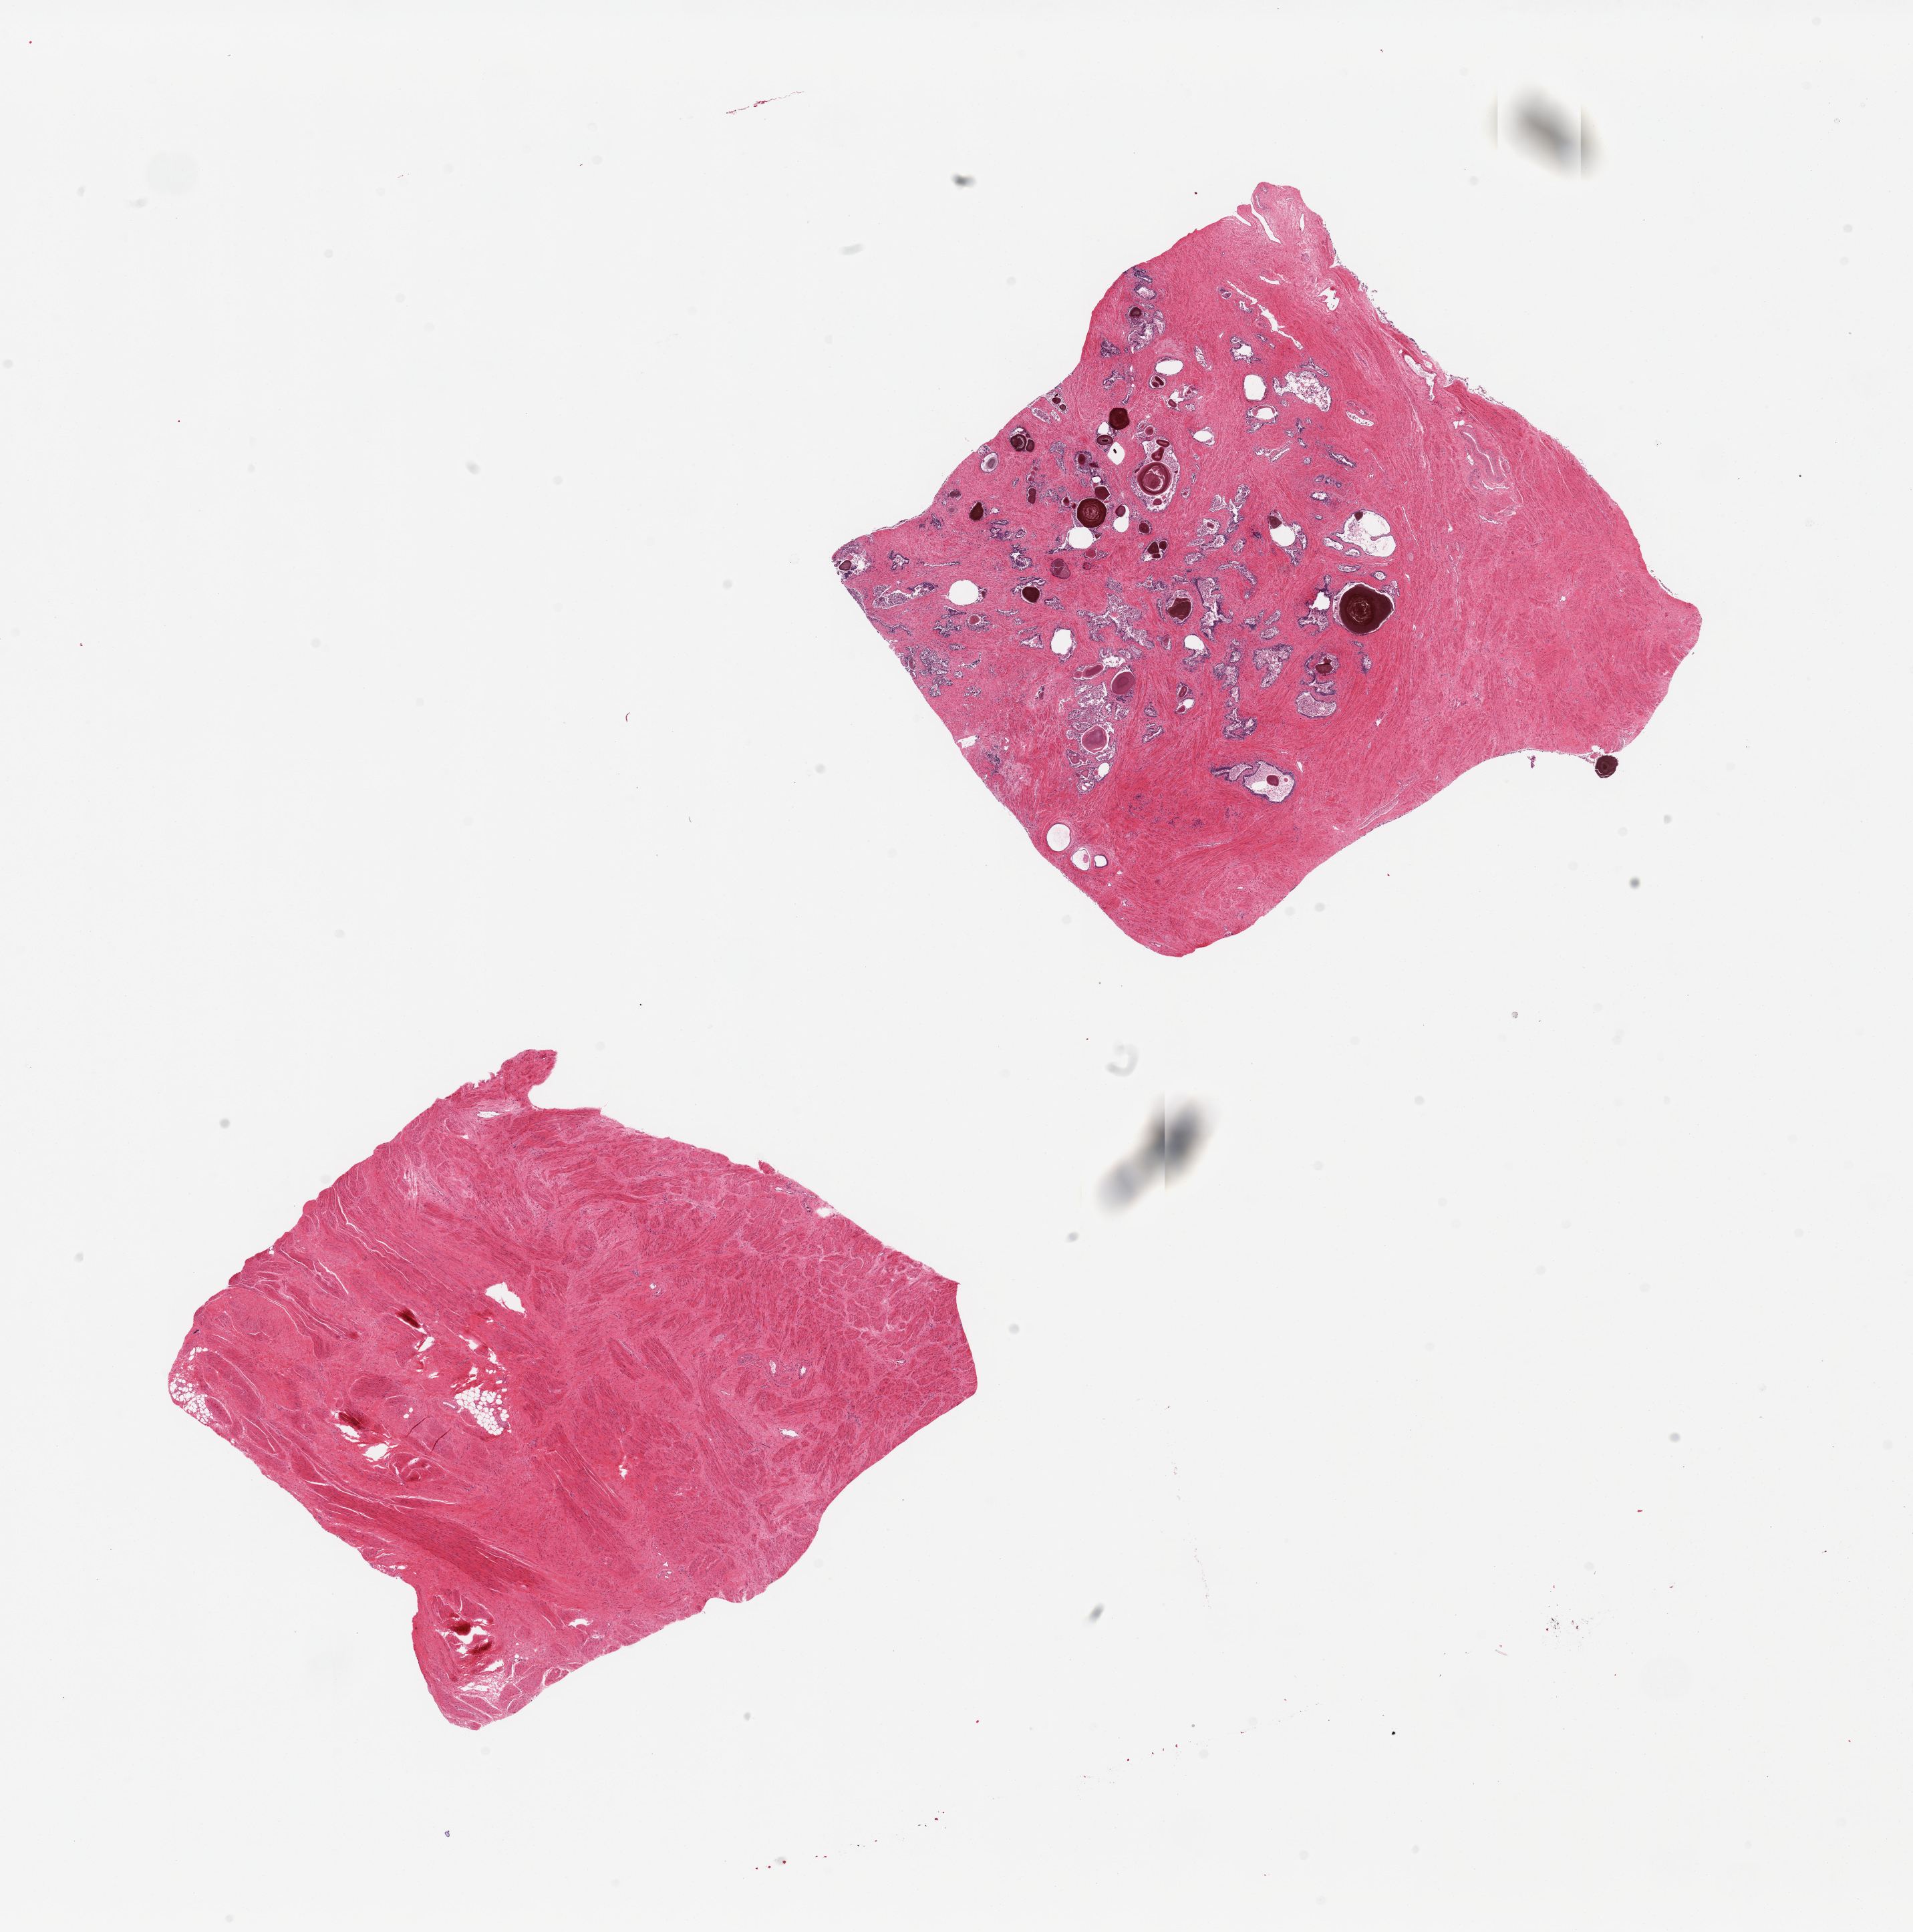
Whole-slide image, H&E stain, brightfield — shown as a low-resolution overview of the whole scanned area (about 22.6 x 22.9 mm, from a 20x scan), PAXgene-fixed paraffin-embedded (PFPE) section, sampled site (target tissue): prostate, donor tissue sample. Male donor.
Pathologist's review note for this sample: 2 pieces; one piece is entirely stroma, second is 25% stroma/75% stroma and glands with sloughing epithelium.